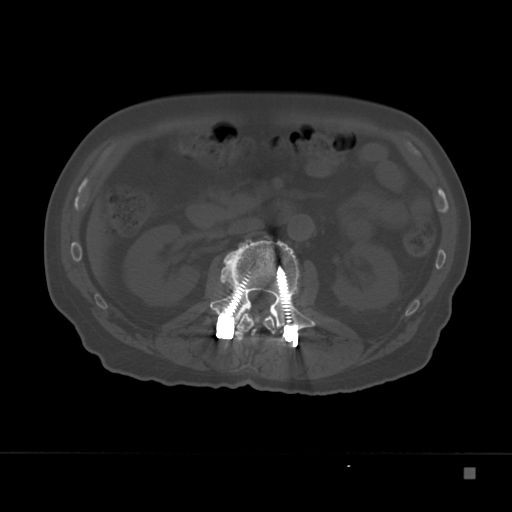
CT including the spine, one axial slice. Position 95 of 332 along the scan axis. Reconstruction kernel Br40s. 120 kVp. Bone window (W 1800 / L 400 HU). 1.5 mm slice thickness. 512 × 512 image matrix, field of view 389 × 389 mm. Male patient, age 72 years. Case-level facts recorded for this patient, not image findings: primary cancer: skeletal.
Structures marked on this image (semi-automatically segmented with operator editing):
- L1 vertebra: bounding box [x1, y1, x2, y2] px = [237, 311, 276, 334]
- L2 vertebra: [209, 237, 316, 330]